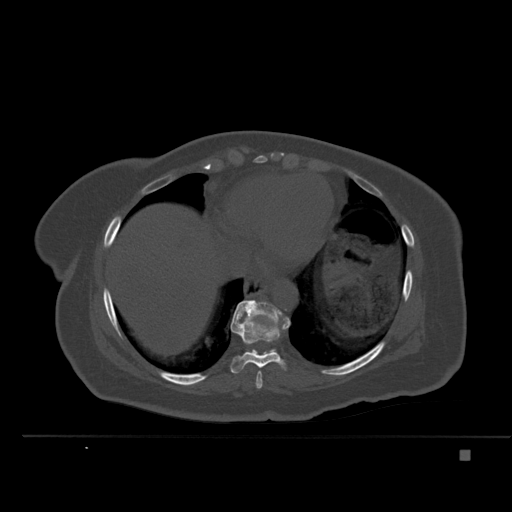
CT including the spine, one axial slice. Position 296 of 477 along the scan axis. Bone window (W 1800 / L 400 HU). 1.5 mm slice thickness. 512 × 512 image matrix, field of view 422 × 422 mm. Female patient, age 74 years. From the clinical record (not read from this slice): primary cancer: colon.
Annotated regions visible in this slice (semi-automatic segmentation, software-assisted and operator-edited):
- T10 vertebra: box from (x=240, y=300) to (x=282, y=352) px
- T8 vertebra: (x=255, y=371)–(x=263, y=389)
- T9 vertebra: (x=230, y=300)–(x=291, y=374)